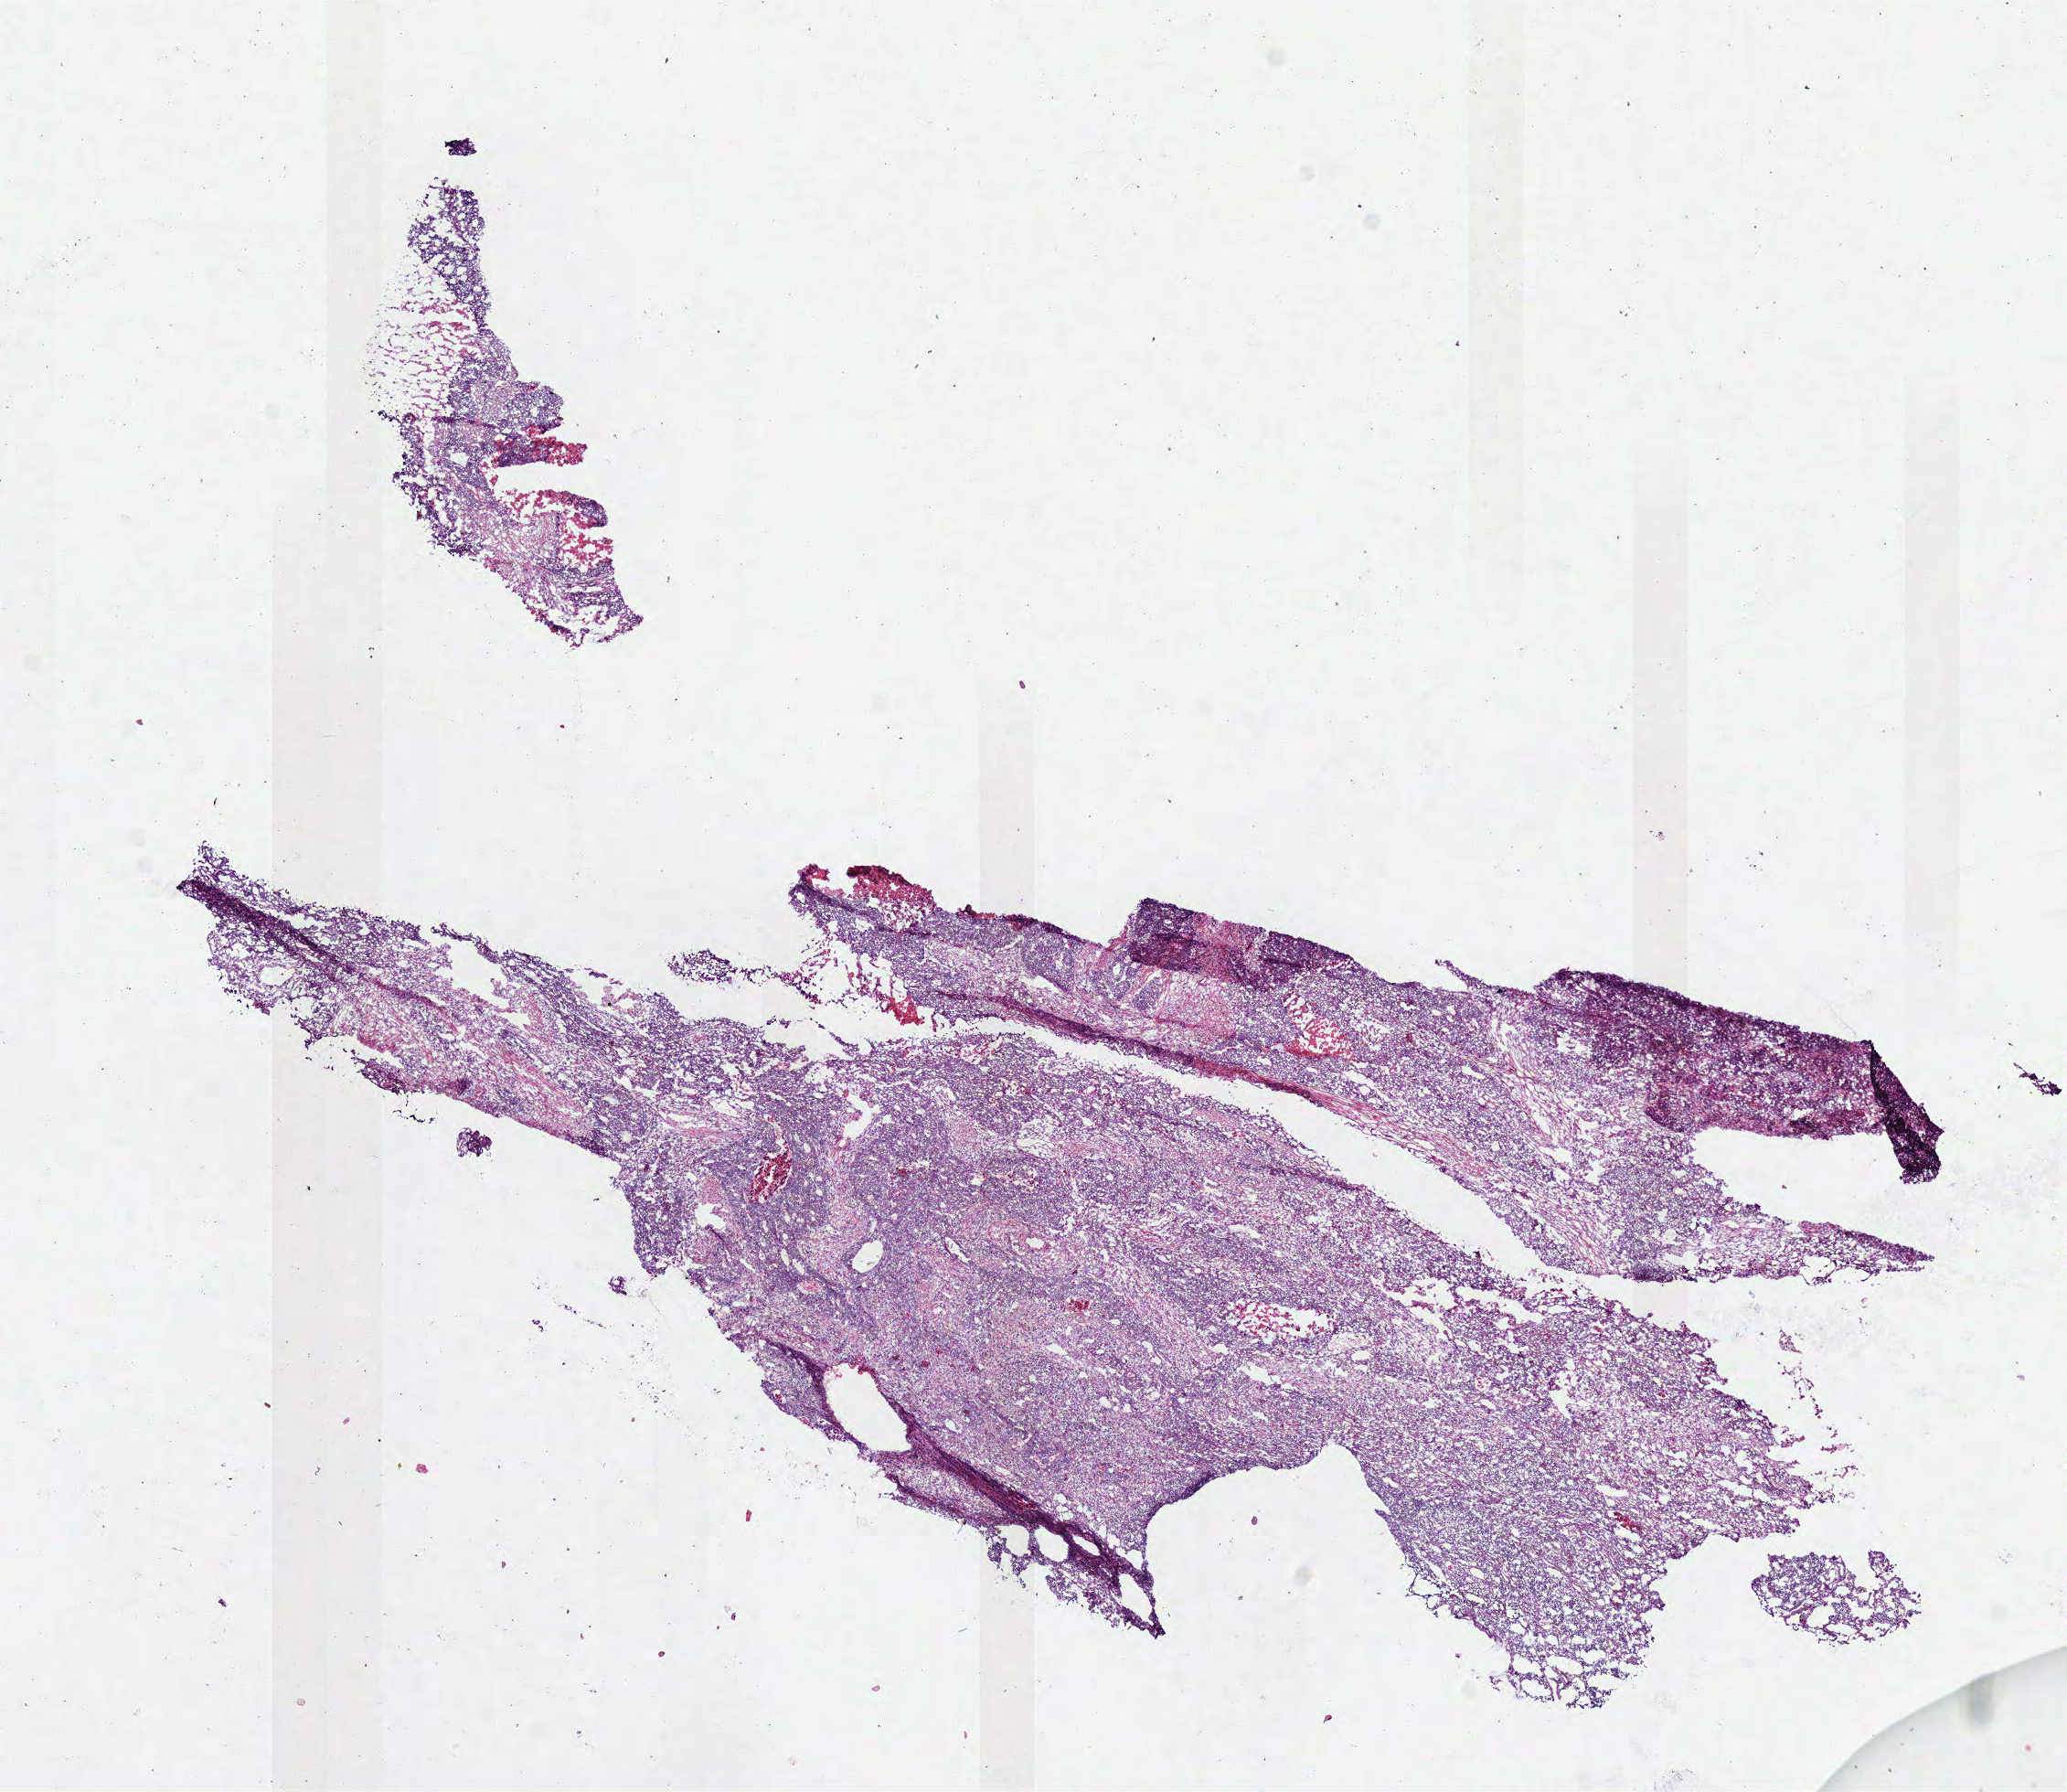
Digitized Hematoxylin and eosin (H&E) stained tissue section (whole slide) — a low-resolution overview of the entire scanned area, about 8.9 x 7.7 mm (from a 40x scan); frozen section from the bottom of the tissue portion; sample: primary tumour, colon. Male patient; age at initial diagnosis 62 years.
Diagnosis: Adenocarcinoma, NOS (cecum).